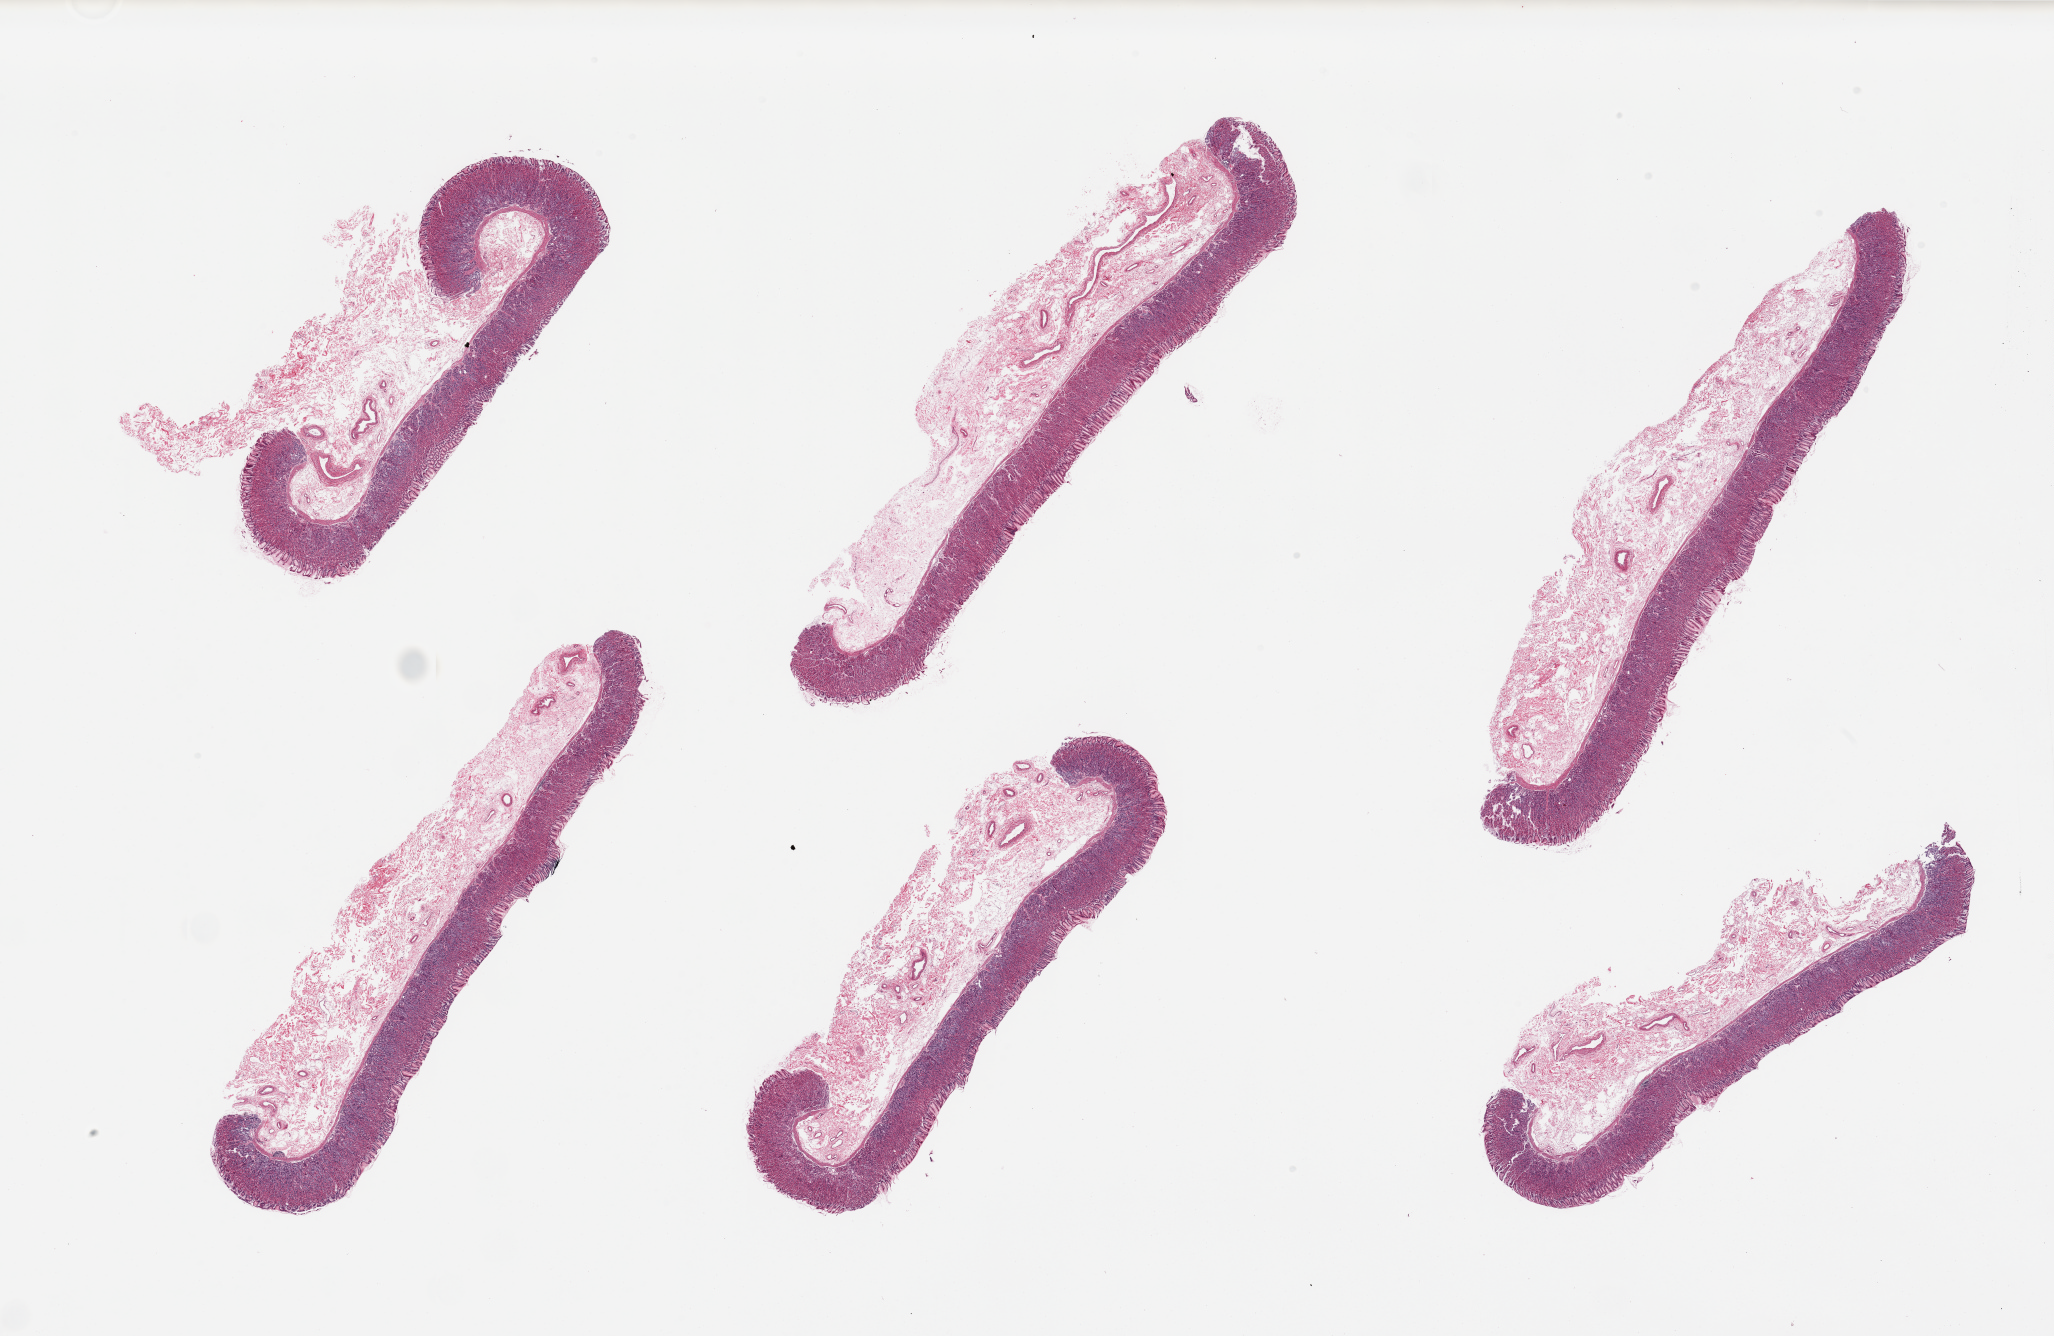
H&E whole-slide image — low-resolution overview of the scanned area, about 32.5 x 21.1 mm, PAXgene-fixed, paraffin-embedded tissue, sampled site (target tissue): stomach, donor tissue sample. Donor: female.
Review note (as recorded): 6 pieces, mucosa and submucosa.